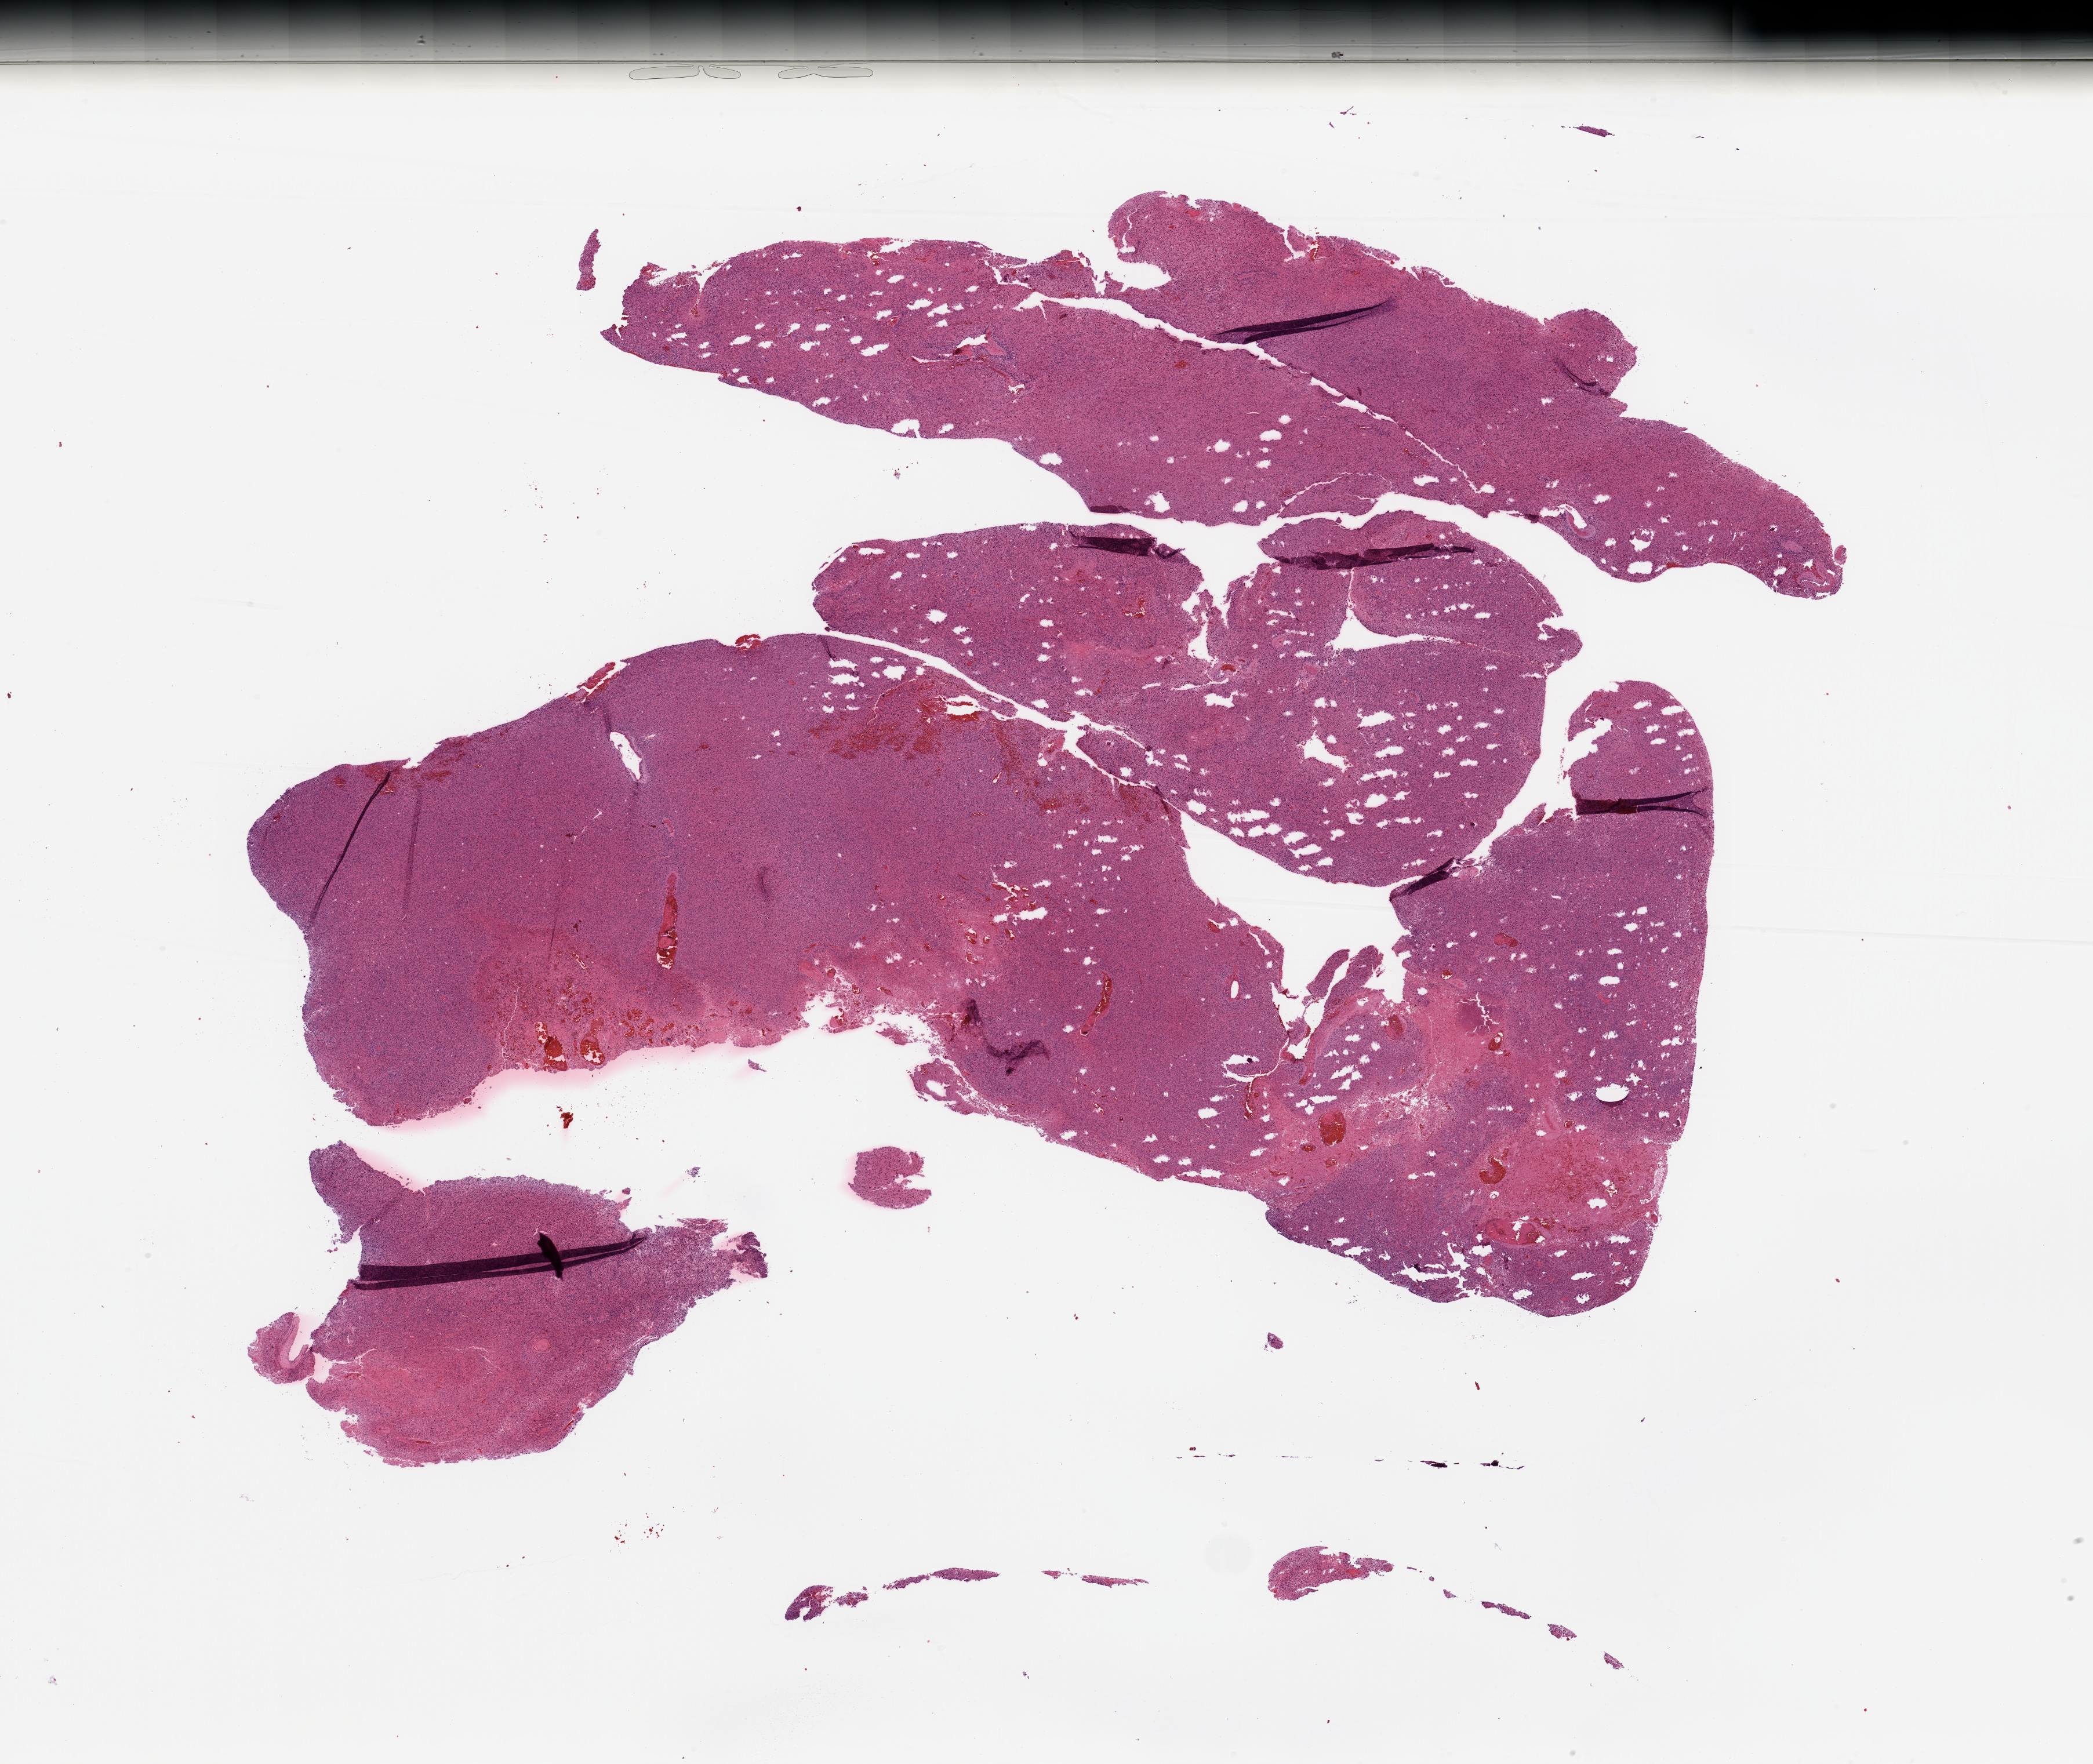
H&E-stained whole-slide image, shown as a low-resolution overview of the whole scanned area (about 28.5 x 24.1 mm). Brain, tumour tissue. Patient: female, age 63 years.
Histologic diagnosis: Glioblastoma.